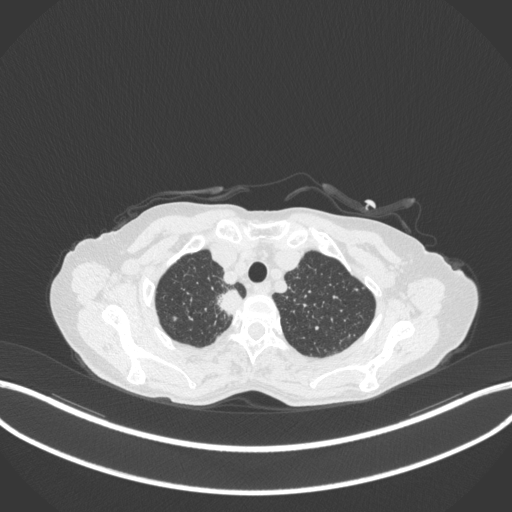
Chest CT, one axial slice. Position 323 of 363 along the scan axis. Reconstruction kernel B31f. 120 kVp. Lung window (W 1500 / L -600 HU). 512 × 512 image matrix, field of view 400 × 400 mm. Female patient, age 75 years. From the clinical record (not read from this slice): clinical TNM (as recorded): T1c N1 M1.
Annotated regions visible in this slice (bounding box drawn by a radiologist):
- lung tumour (recorded histology: adenocarcinoma): bounding box <215,286,248,321> (left, top, right, bottom; pixels)